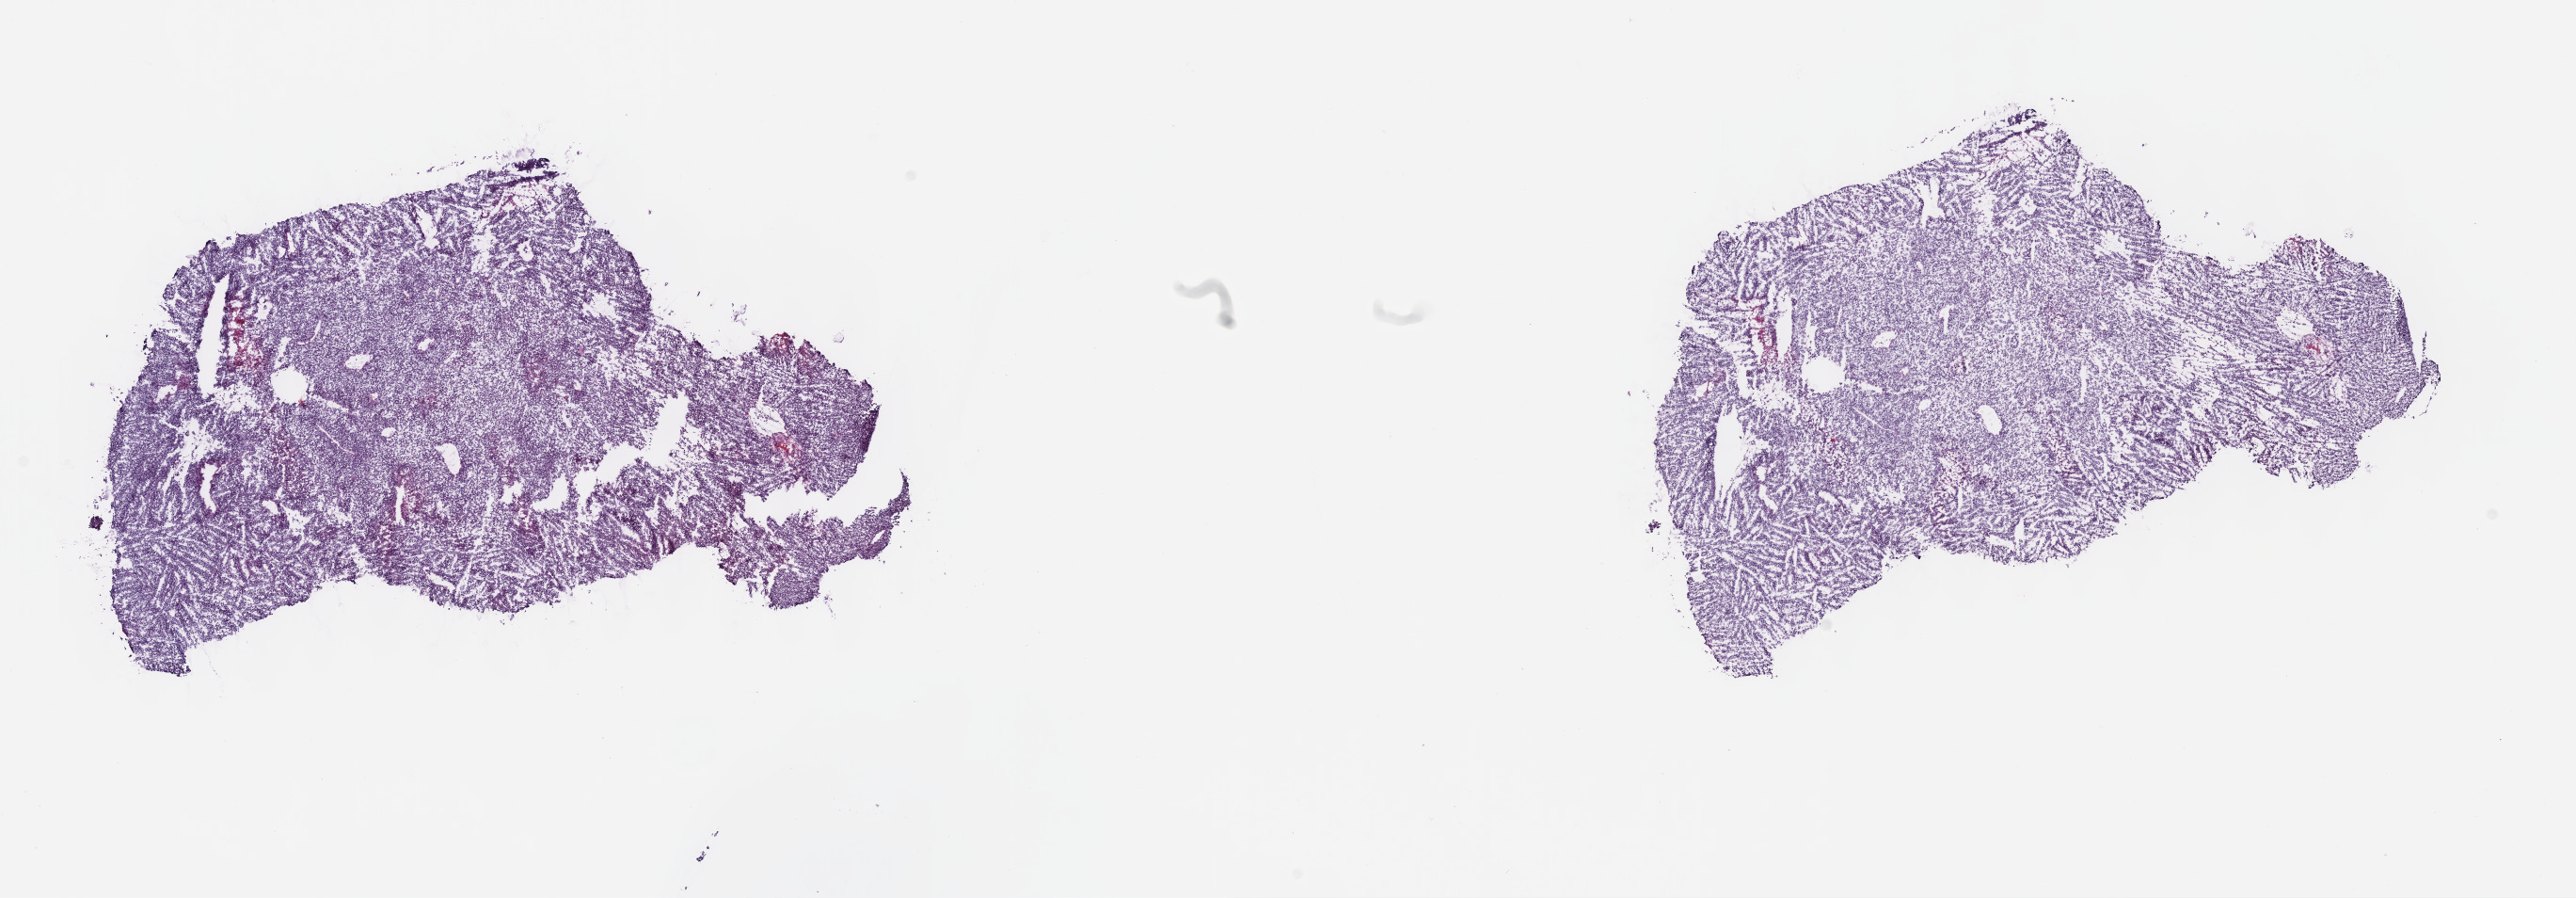
Hematoxylin and eosin (H&E) stained whole-slide image, shown as a low-resolution overview of the whole scanned area (about 22.1 x 7.7 mm, from a 40x scan), frozen section, metastatic tumour sample, sampled site: liver. Patient: female, age at initial diagnosis 43 years. Composition of this section per pathologist review: tumour cells 96%, tumour nuclei 80%, normal cells 0%, stromal cells 0%, necrosis 4%. Infiltration values recorded for this section: lymphocyte infiltration 2%, monocyte infiltration 0%, neutrophil infiltration 0%.
* this section: metastatic tumour tissue
* patient diagnosis: Malignant melanoma, NOS